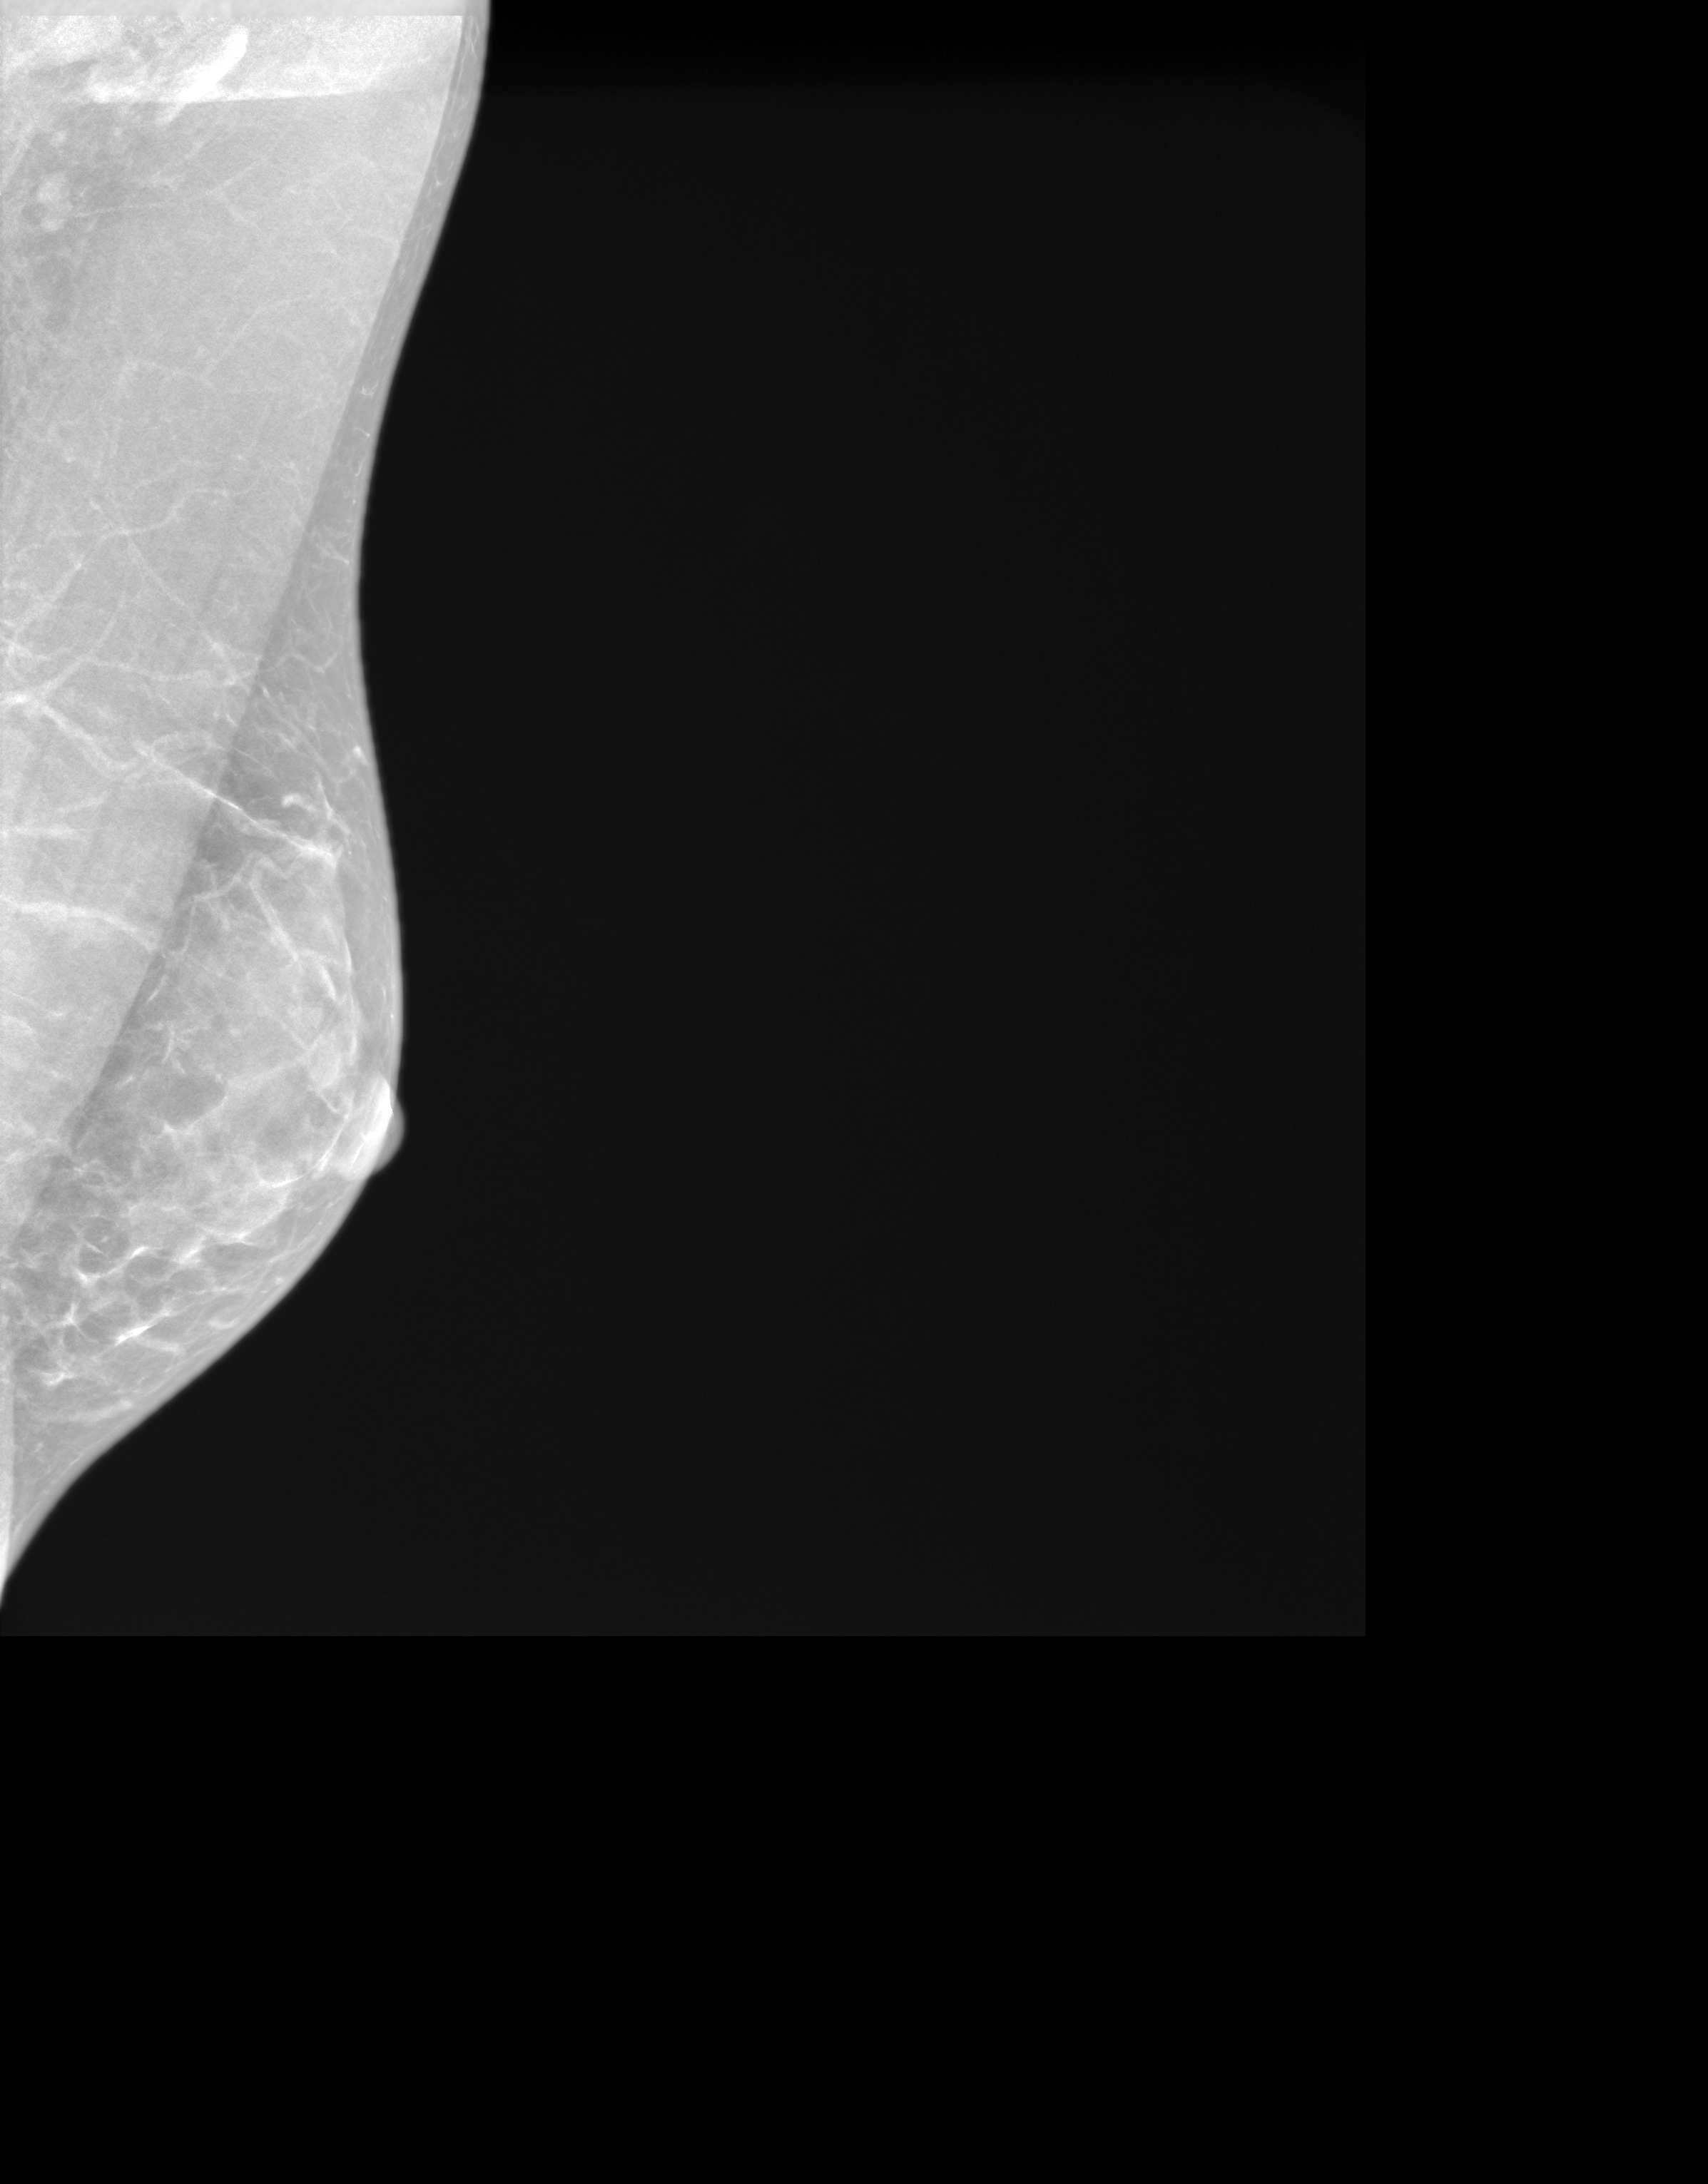
Synthetic 2-D view generated from a tomosynthesis acquisition (not an FFDM exposure), left breast, medio-lateral oblique projection, annual screening mammography examination. Female patient, age 55 years.
- BI-RADS breast density category at the screening exam (both breasts, scale 1–4): 4
- final BI-RADS assessment for this screening round (tomosynthesis exam, both breasts): category 1
- recall: no recall after this screen